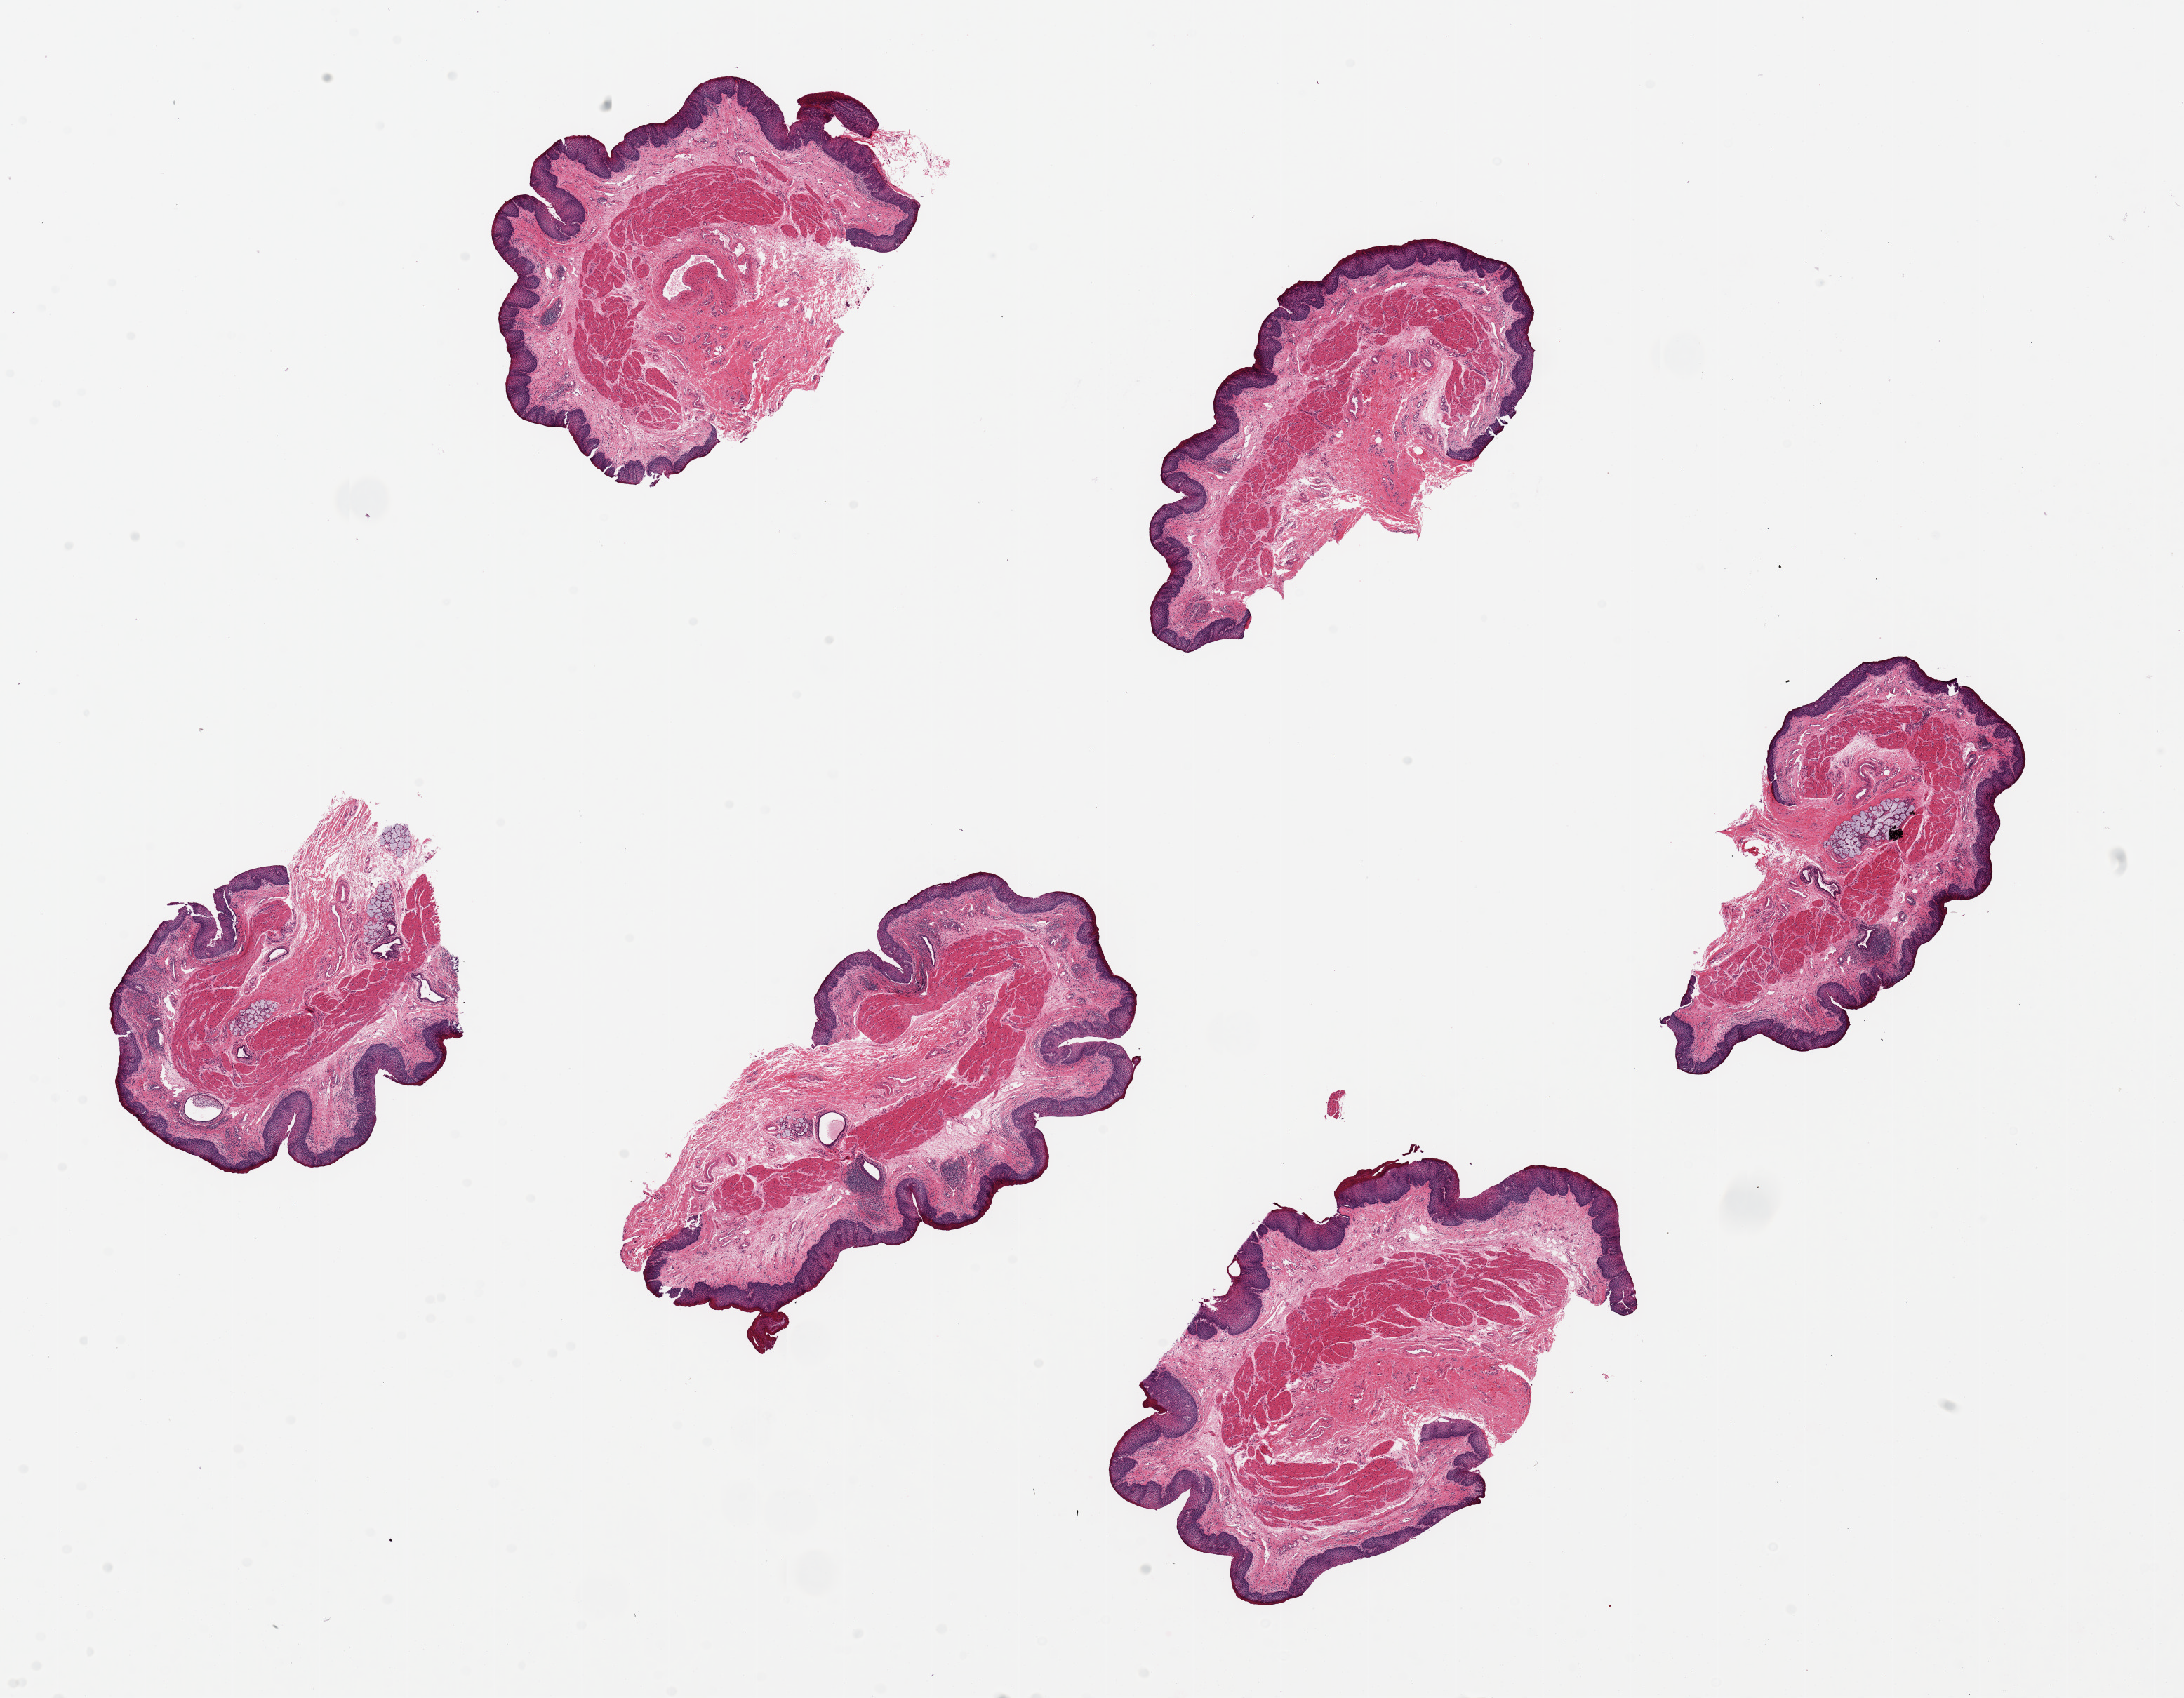
Hematoxylin and eosin (H&E) whole-slide image, low-resolution overview of the scanned area, about 24.6 x 19.1 mm. PAXgene-fixed, paraffin-embedded tissue. Target tissue: esophageal mucous membrane. Tissue donor sample. Donor: male.
• reviewer comment on this tissue sample: 6 pieces, up to 6x4mm; well sampled and well preserved mucosa with focal chronic esophagitis